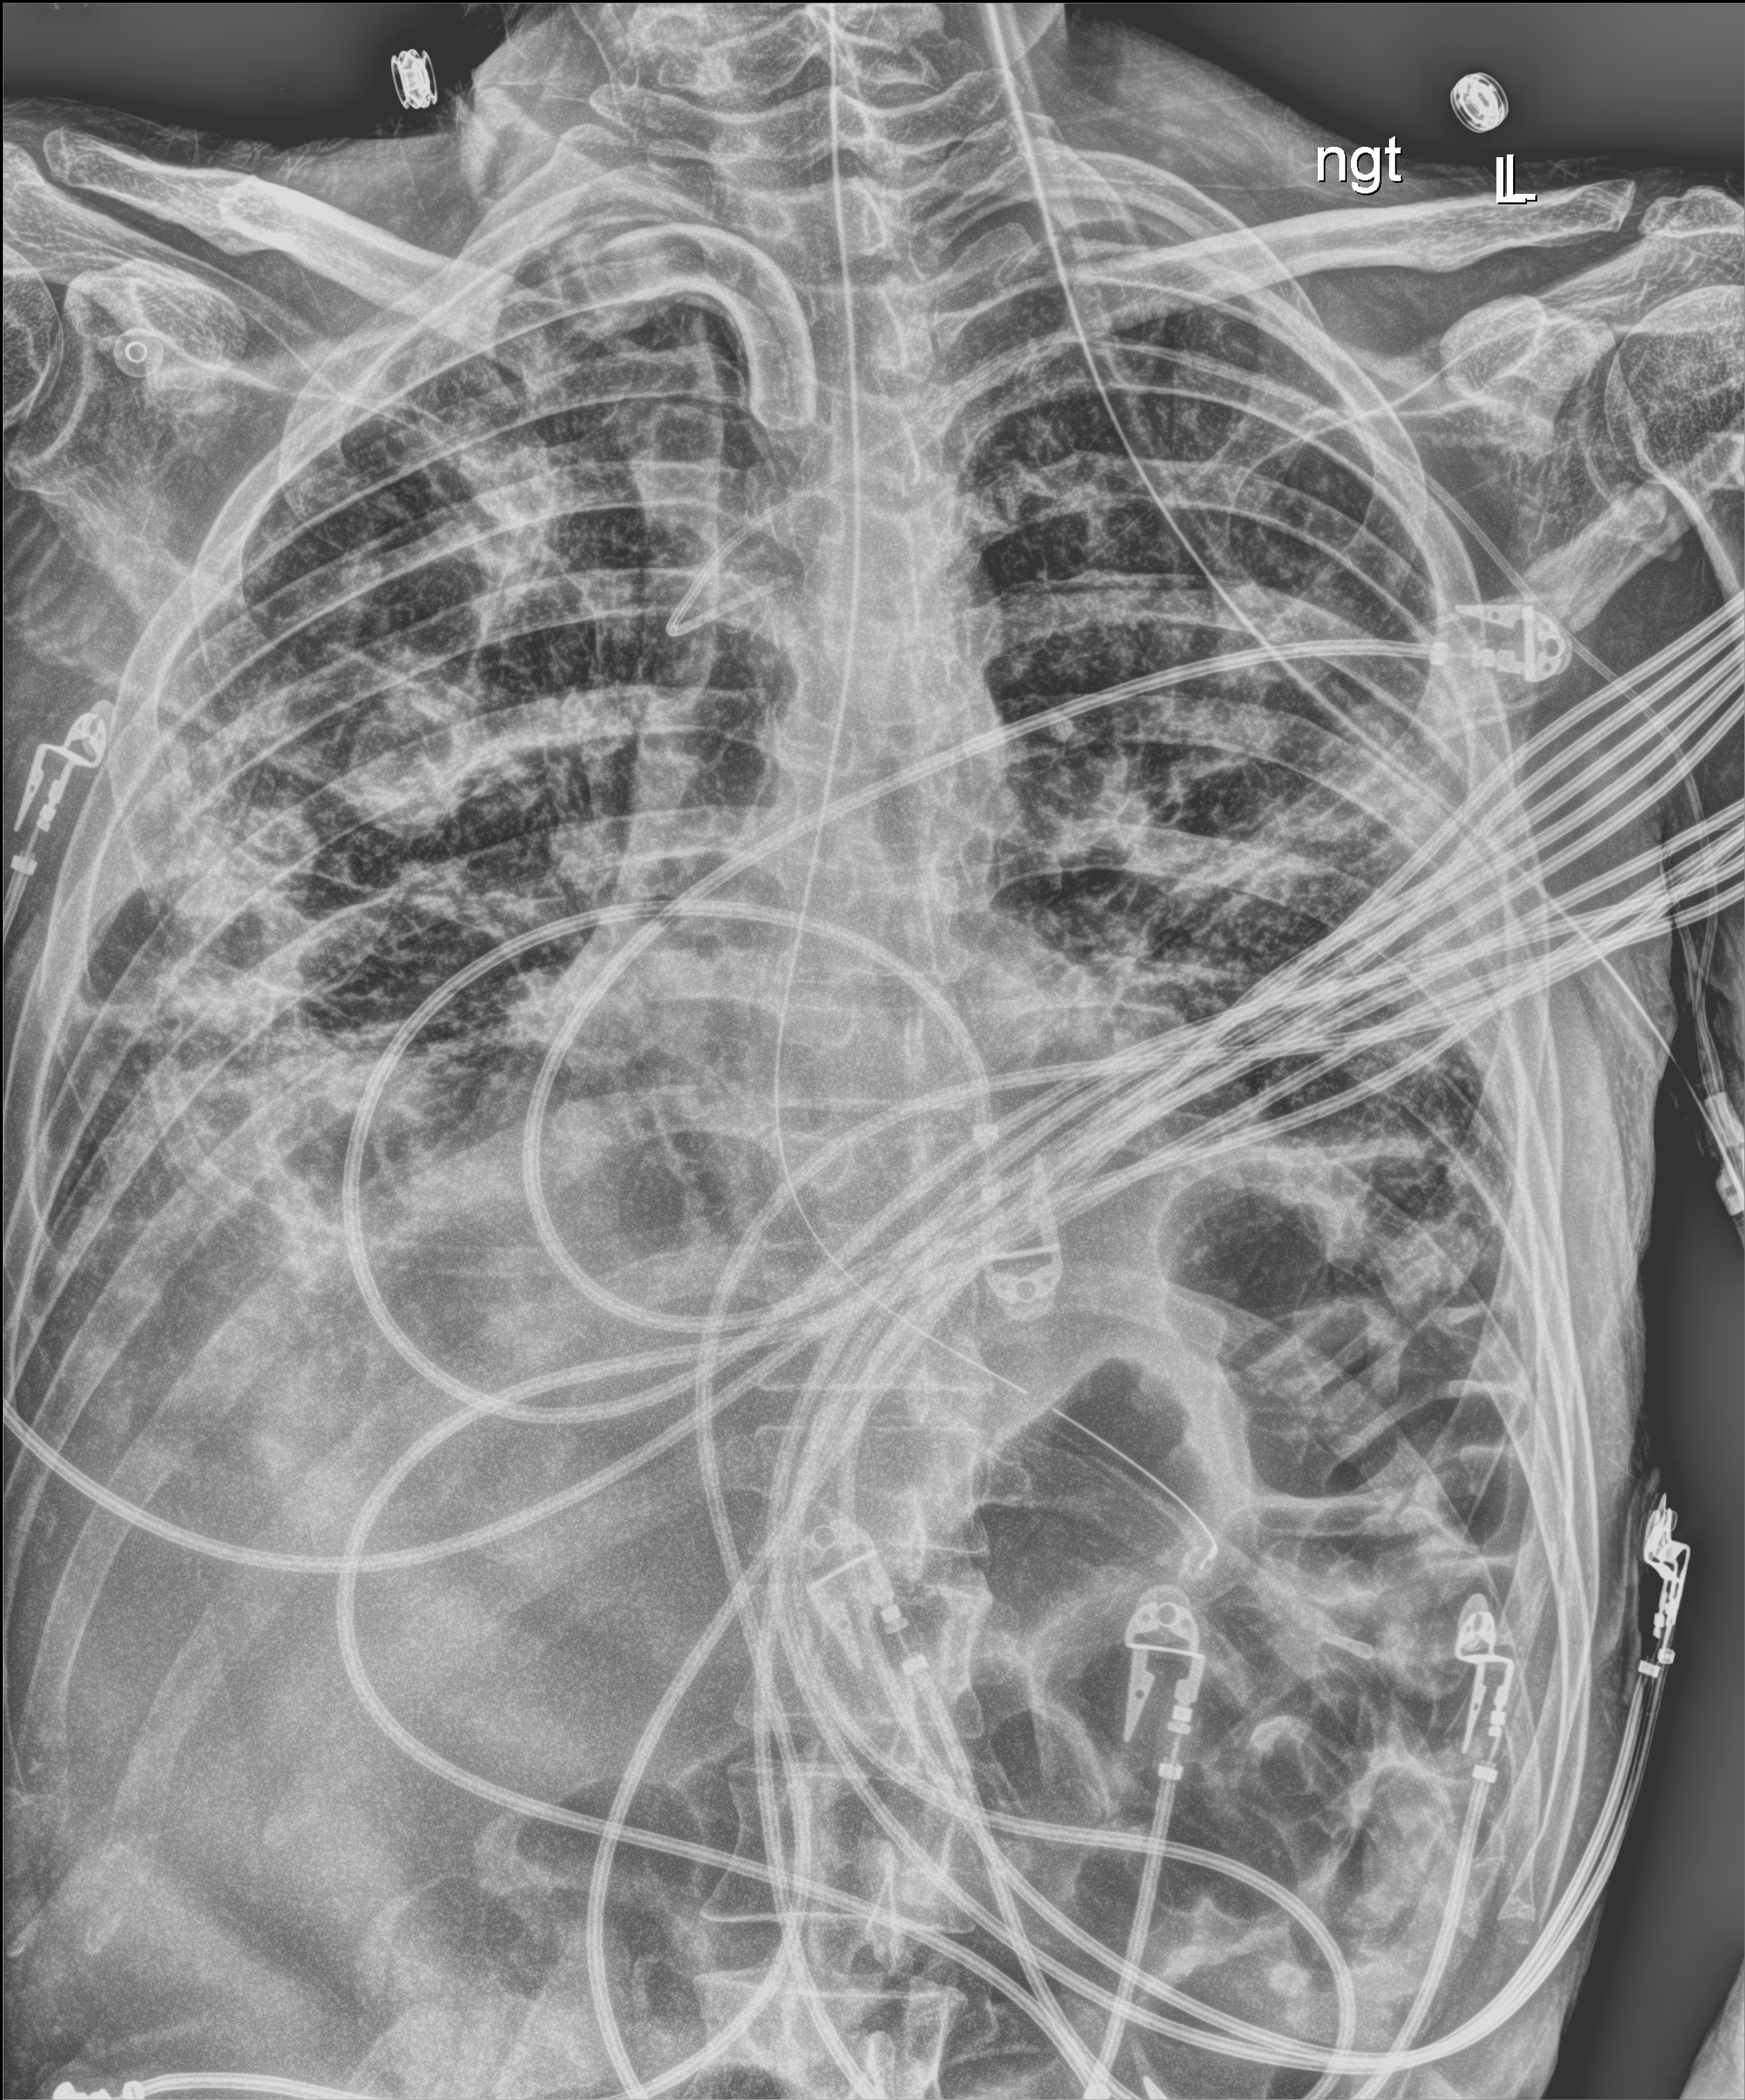
Chest X-ray (portable), anteroposterior (AP) projection. Male patient hospitalised with COVID-19, age 18–59 years.
From the hospital-stay record, not from the radiograph (when in the stay this image was taken is not recorded): admitted to intensive care during this hospital stay: yes.